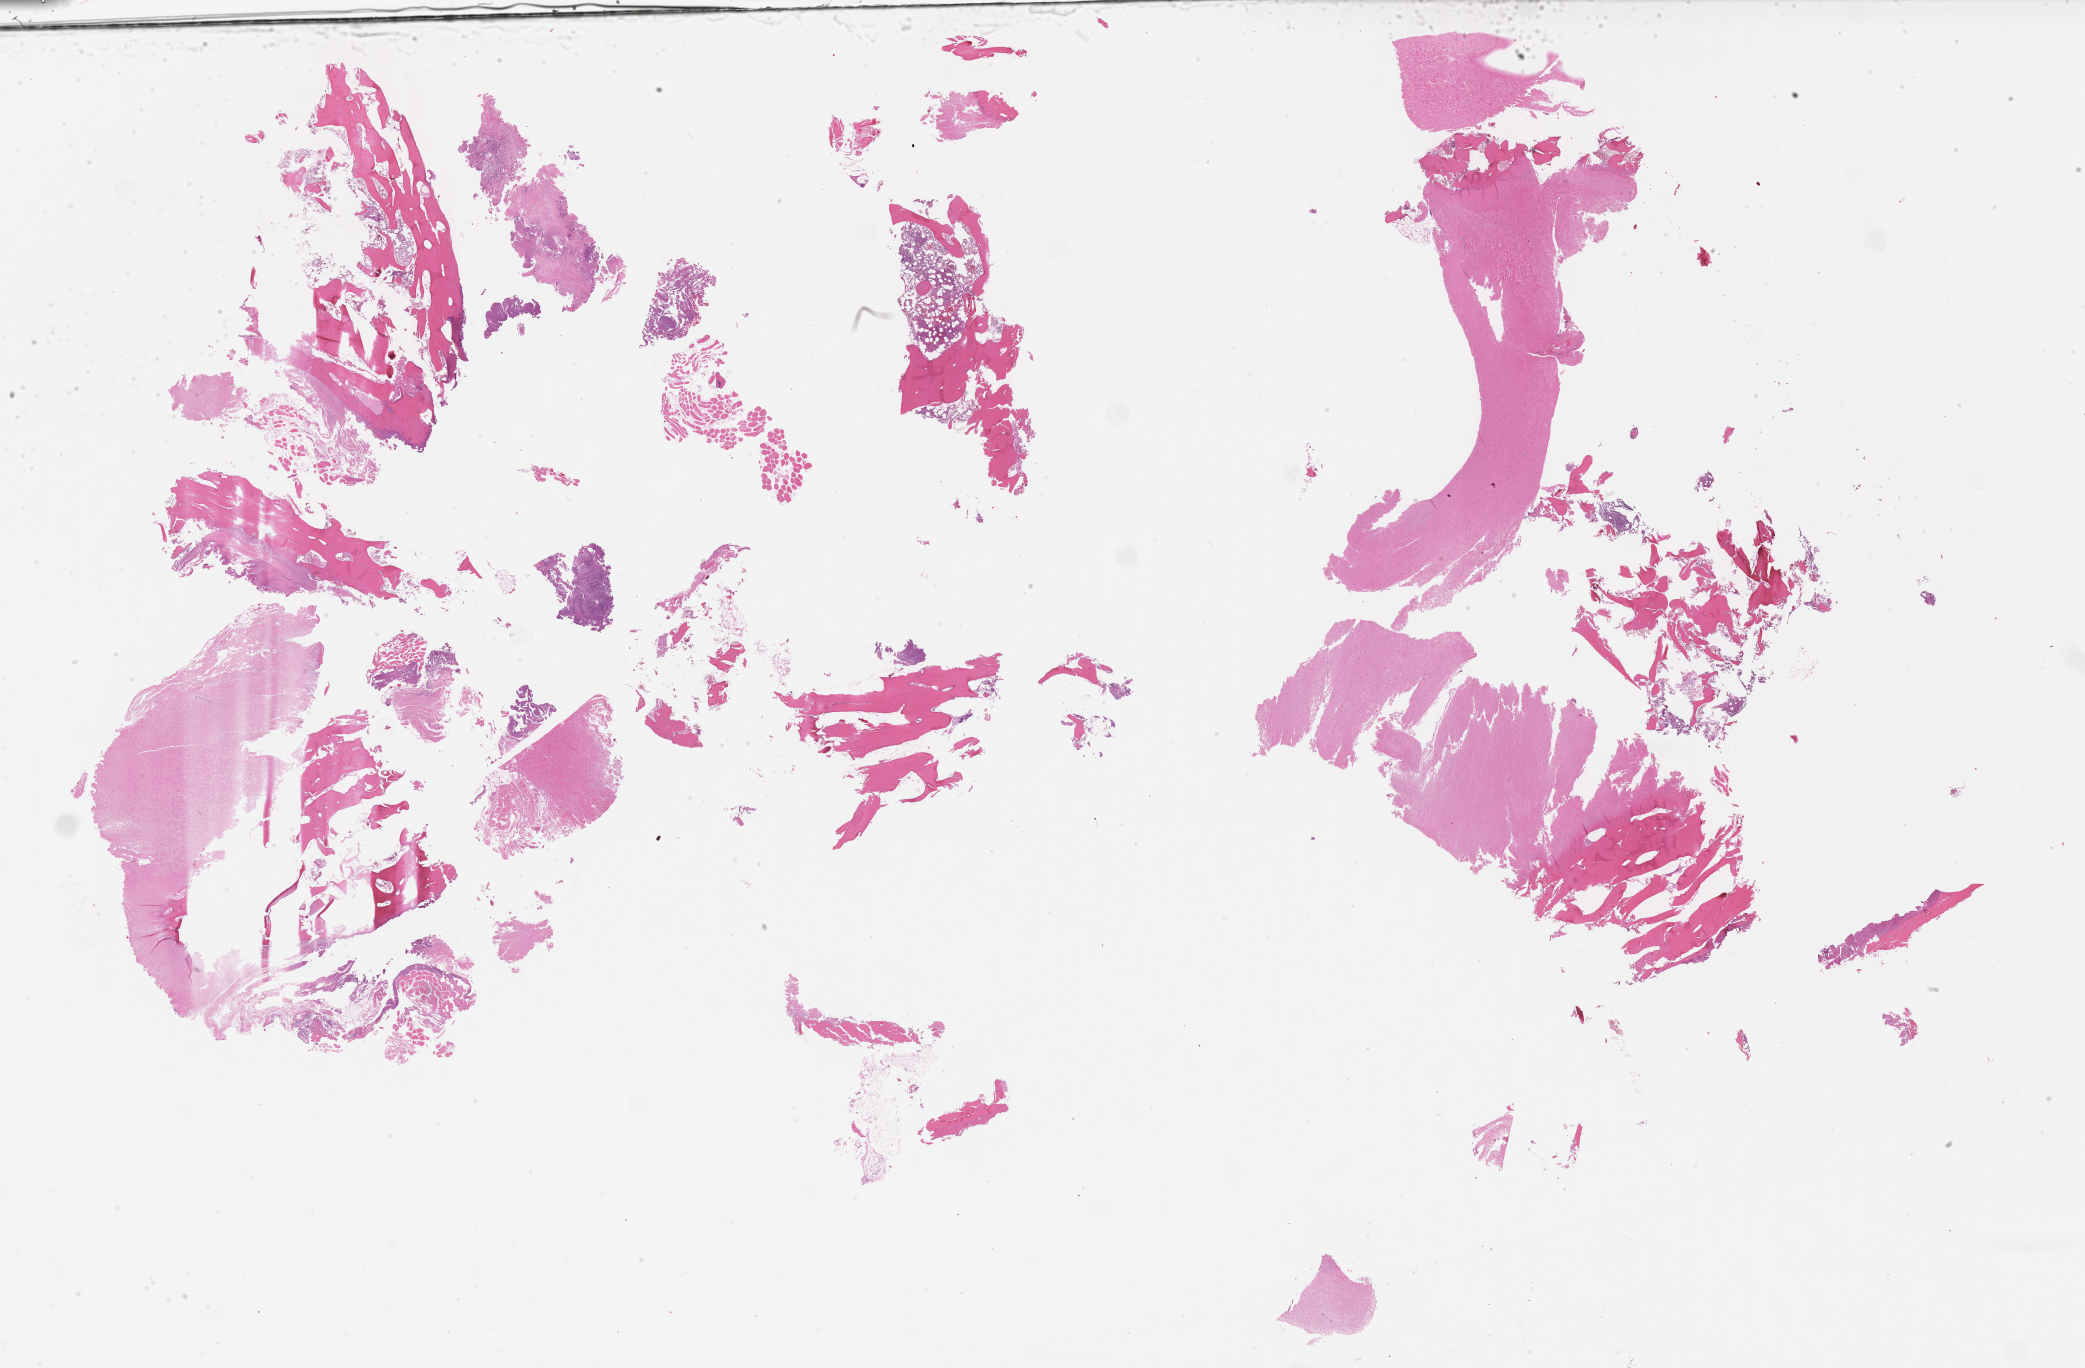
Whole-slide image, haematoxylin and eosin stain of tumor tissue, a low-resolution overview of the entire scanned area, about 33.7 x 22.1 mm. Formalin-fixed paraffin-embedded section. Site: soft tissue, spine. Patient: female, age 10.9 years at diagnosis.
Diagnosis: rhabdomyosarcoma; histological classification: alveolar rhabdomyosarcoma.